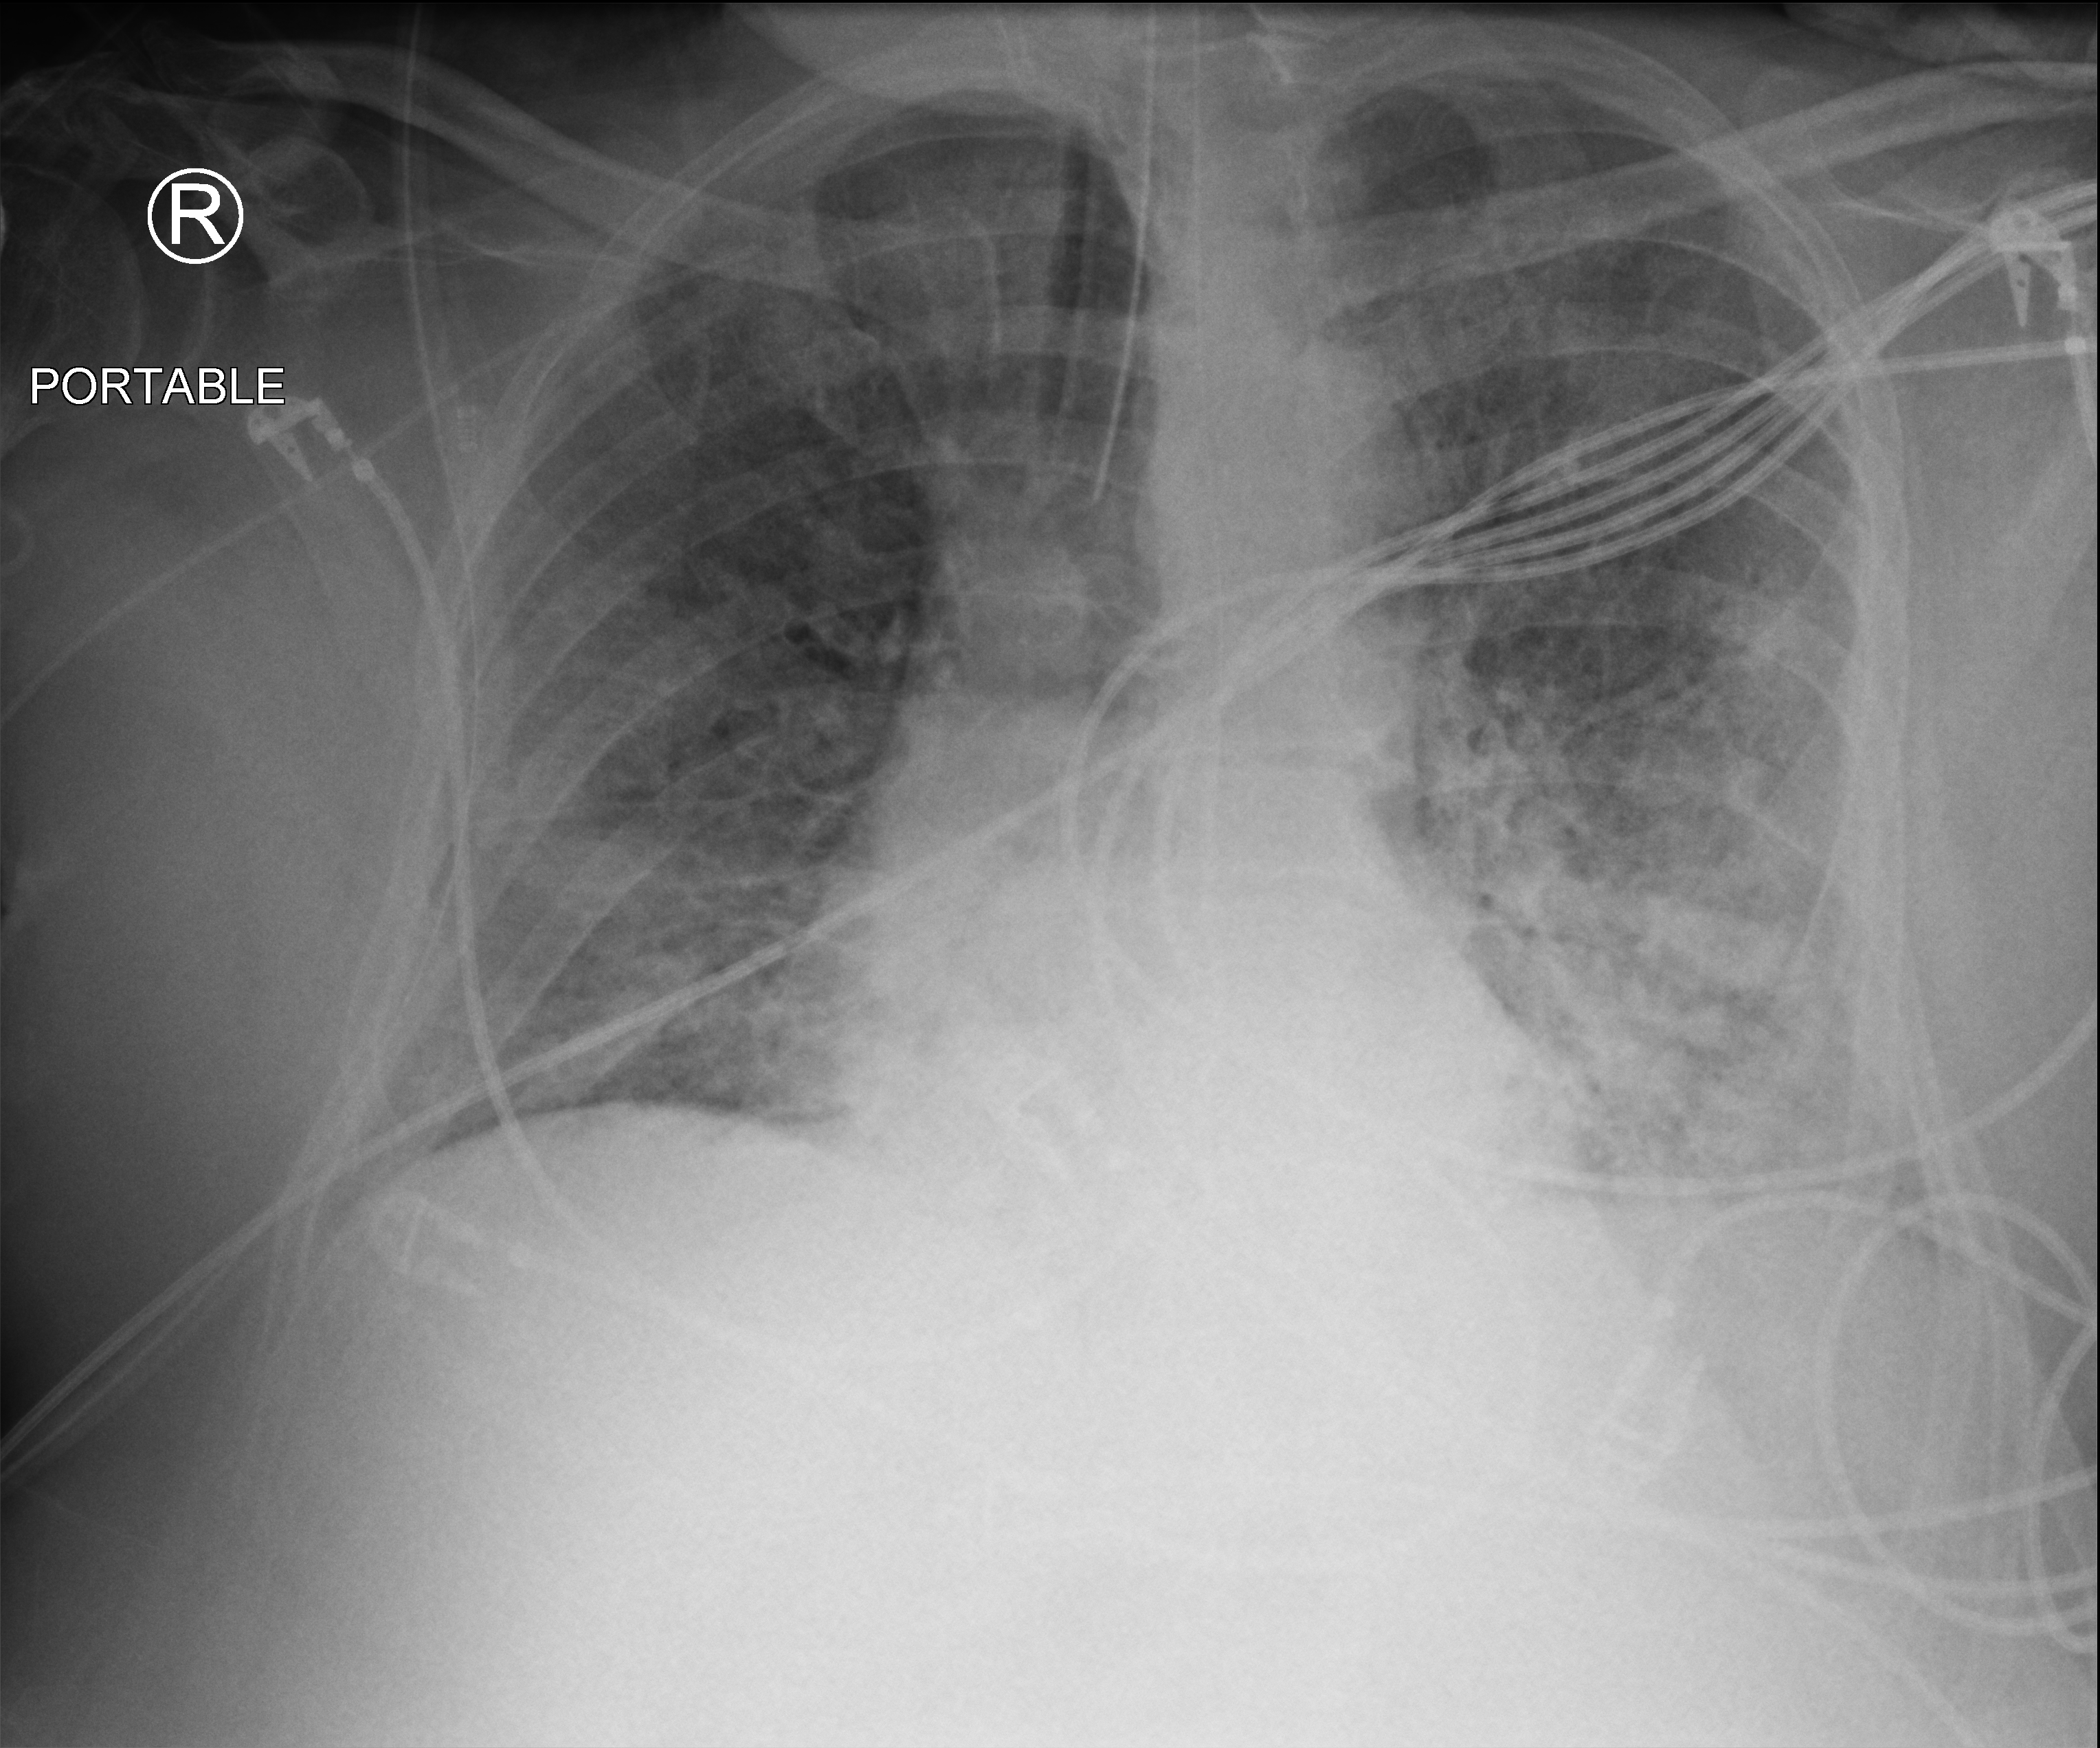
Portable chest radiograph. Patient hospitalised with COVID-19; male, aged 60–74 years.
From the hospital-stay record, not from the radiograph (when in the stay this image was taken is not recorded):
- admitted to intensive care during this hospital stay: yes
- length of hospital stay: 20 days